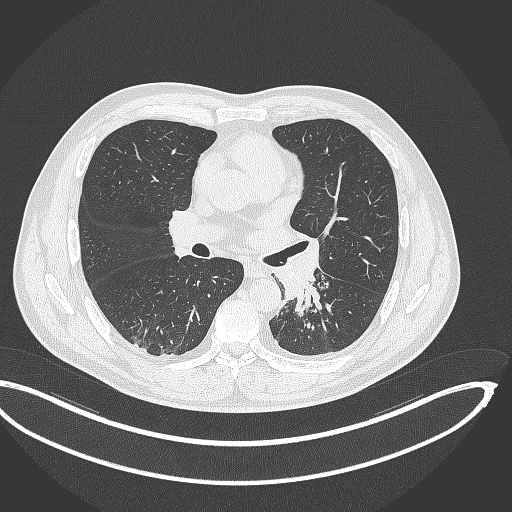
Chest CT, one axial slice. Position 196 of 362 along the scan axis. Lung window (W 1500 / L -600 HU). 1 mm slice thickness. 512 × 512 image matrix. Patient: male, 50 years. From the clinical record (not read from this slice): clinical TNM (as recorded): T2a N3 M0.
Structures marked on this image (rectangle marked by the reading radiologist):
- lung tumour (recorded histology: squamous cell carcinoma): bounding box [x1, y1, x2, y2] px = [282, 275, 324, 317]